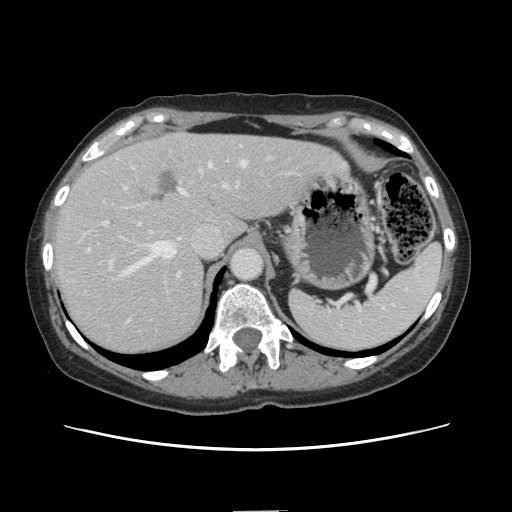
Contrast-enhanced abdominal CT, one axial slice; slice 105 of 141 in the series (ordered by position); 120 kVp; soft-tissue window (W 400 / L 40 HU); 2.5 mm slice thickness; 512 × 512 image matrix, field of view 350 × 350 mm. Female patient, age 63 years. Case-level facts recorded for this patient, not image findings: diagnosis: colorectal cancer liver metastases, imaged before liver resection; multiple liver metastases: yes; largest metastasis: 3.2 cm; disease in both lobes: yes.
Annotated regions visible in this slice (manually delineated by an expert):
- hepatic veins: bounding box (x1, y1, x2, y2) in pixels: (119, 161, 246, 278)
- liver: (53, 133, 344, 355)
- planned liver remnant (the part of the liver to remain after resection): (186, 134, 344, 240)
- portal vein (with intrahepatic branches): (104, 184, 228, 277)